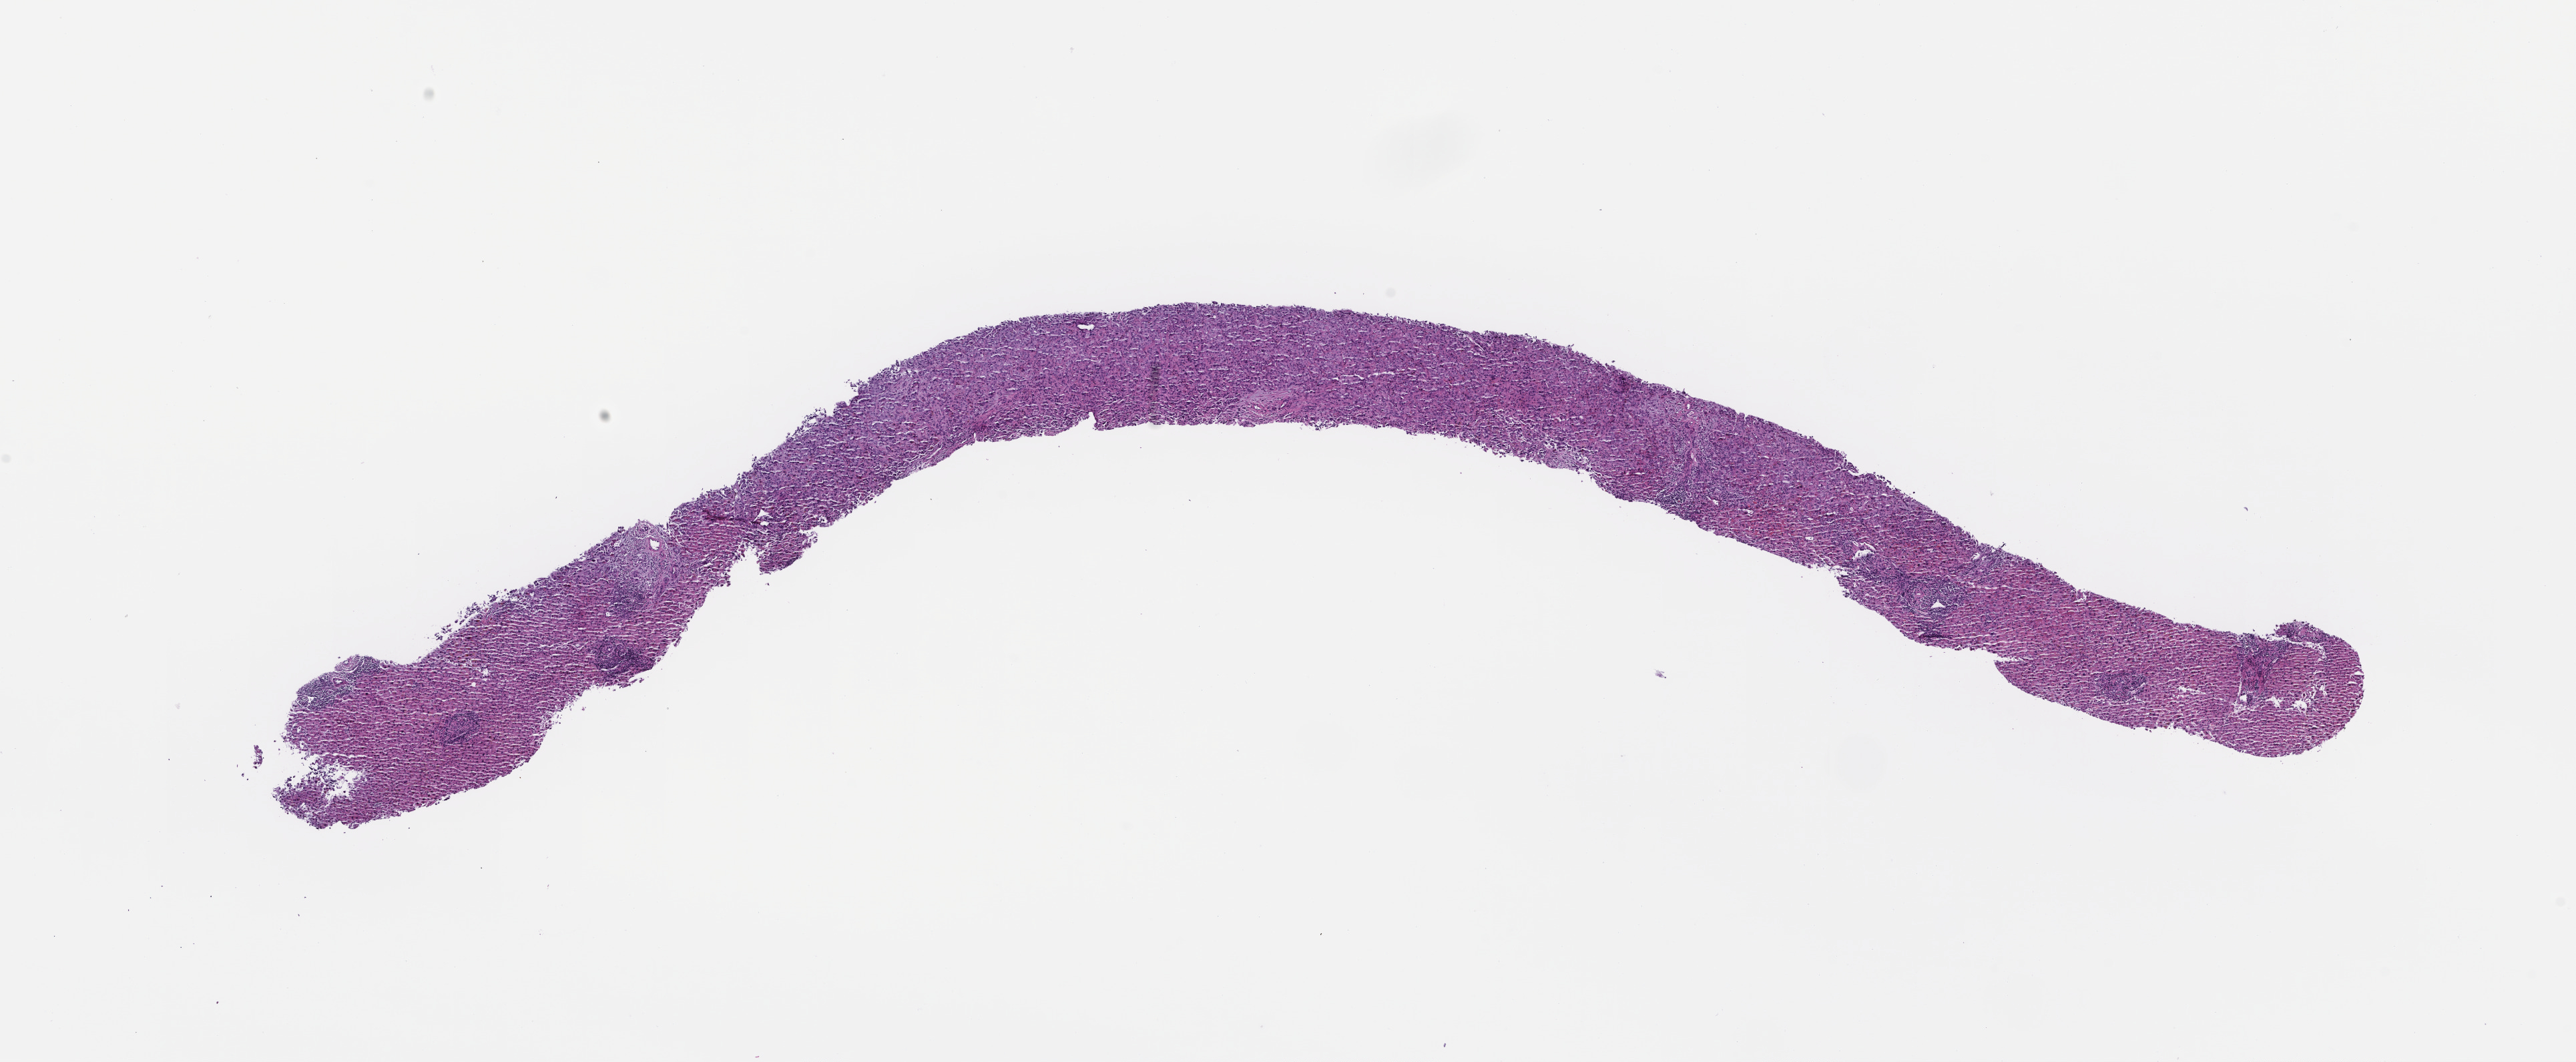
Digitized haematoxylin and eosin-stained section — shown as a low-resolution overview of the whole scanned area (about 15.6 x 6.4 mm), FFPE section, specimen time point: collected at baseline (before treatment). Male patient.
This section: metastatic tumor tissue. Patient diagnosis (primary): Non-Small Cell Lung Carcinoma.